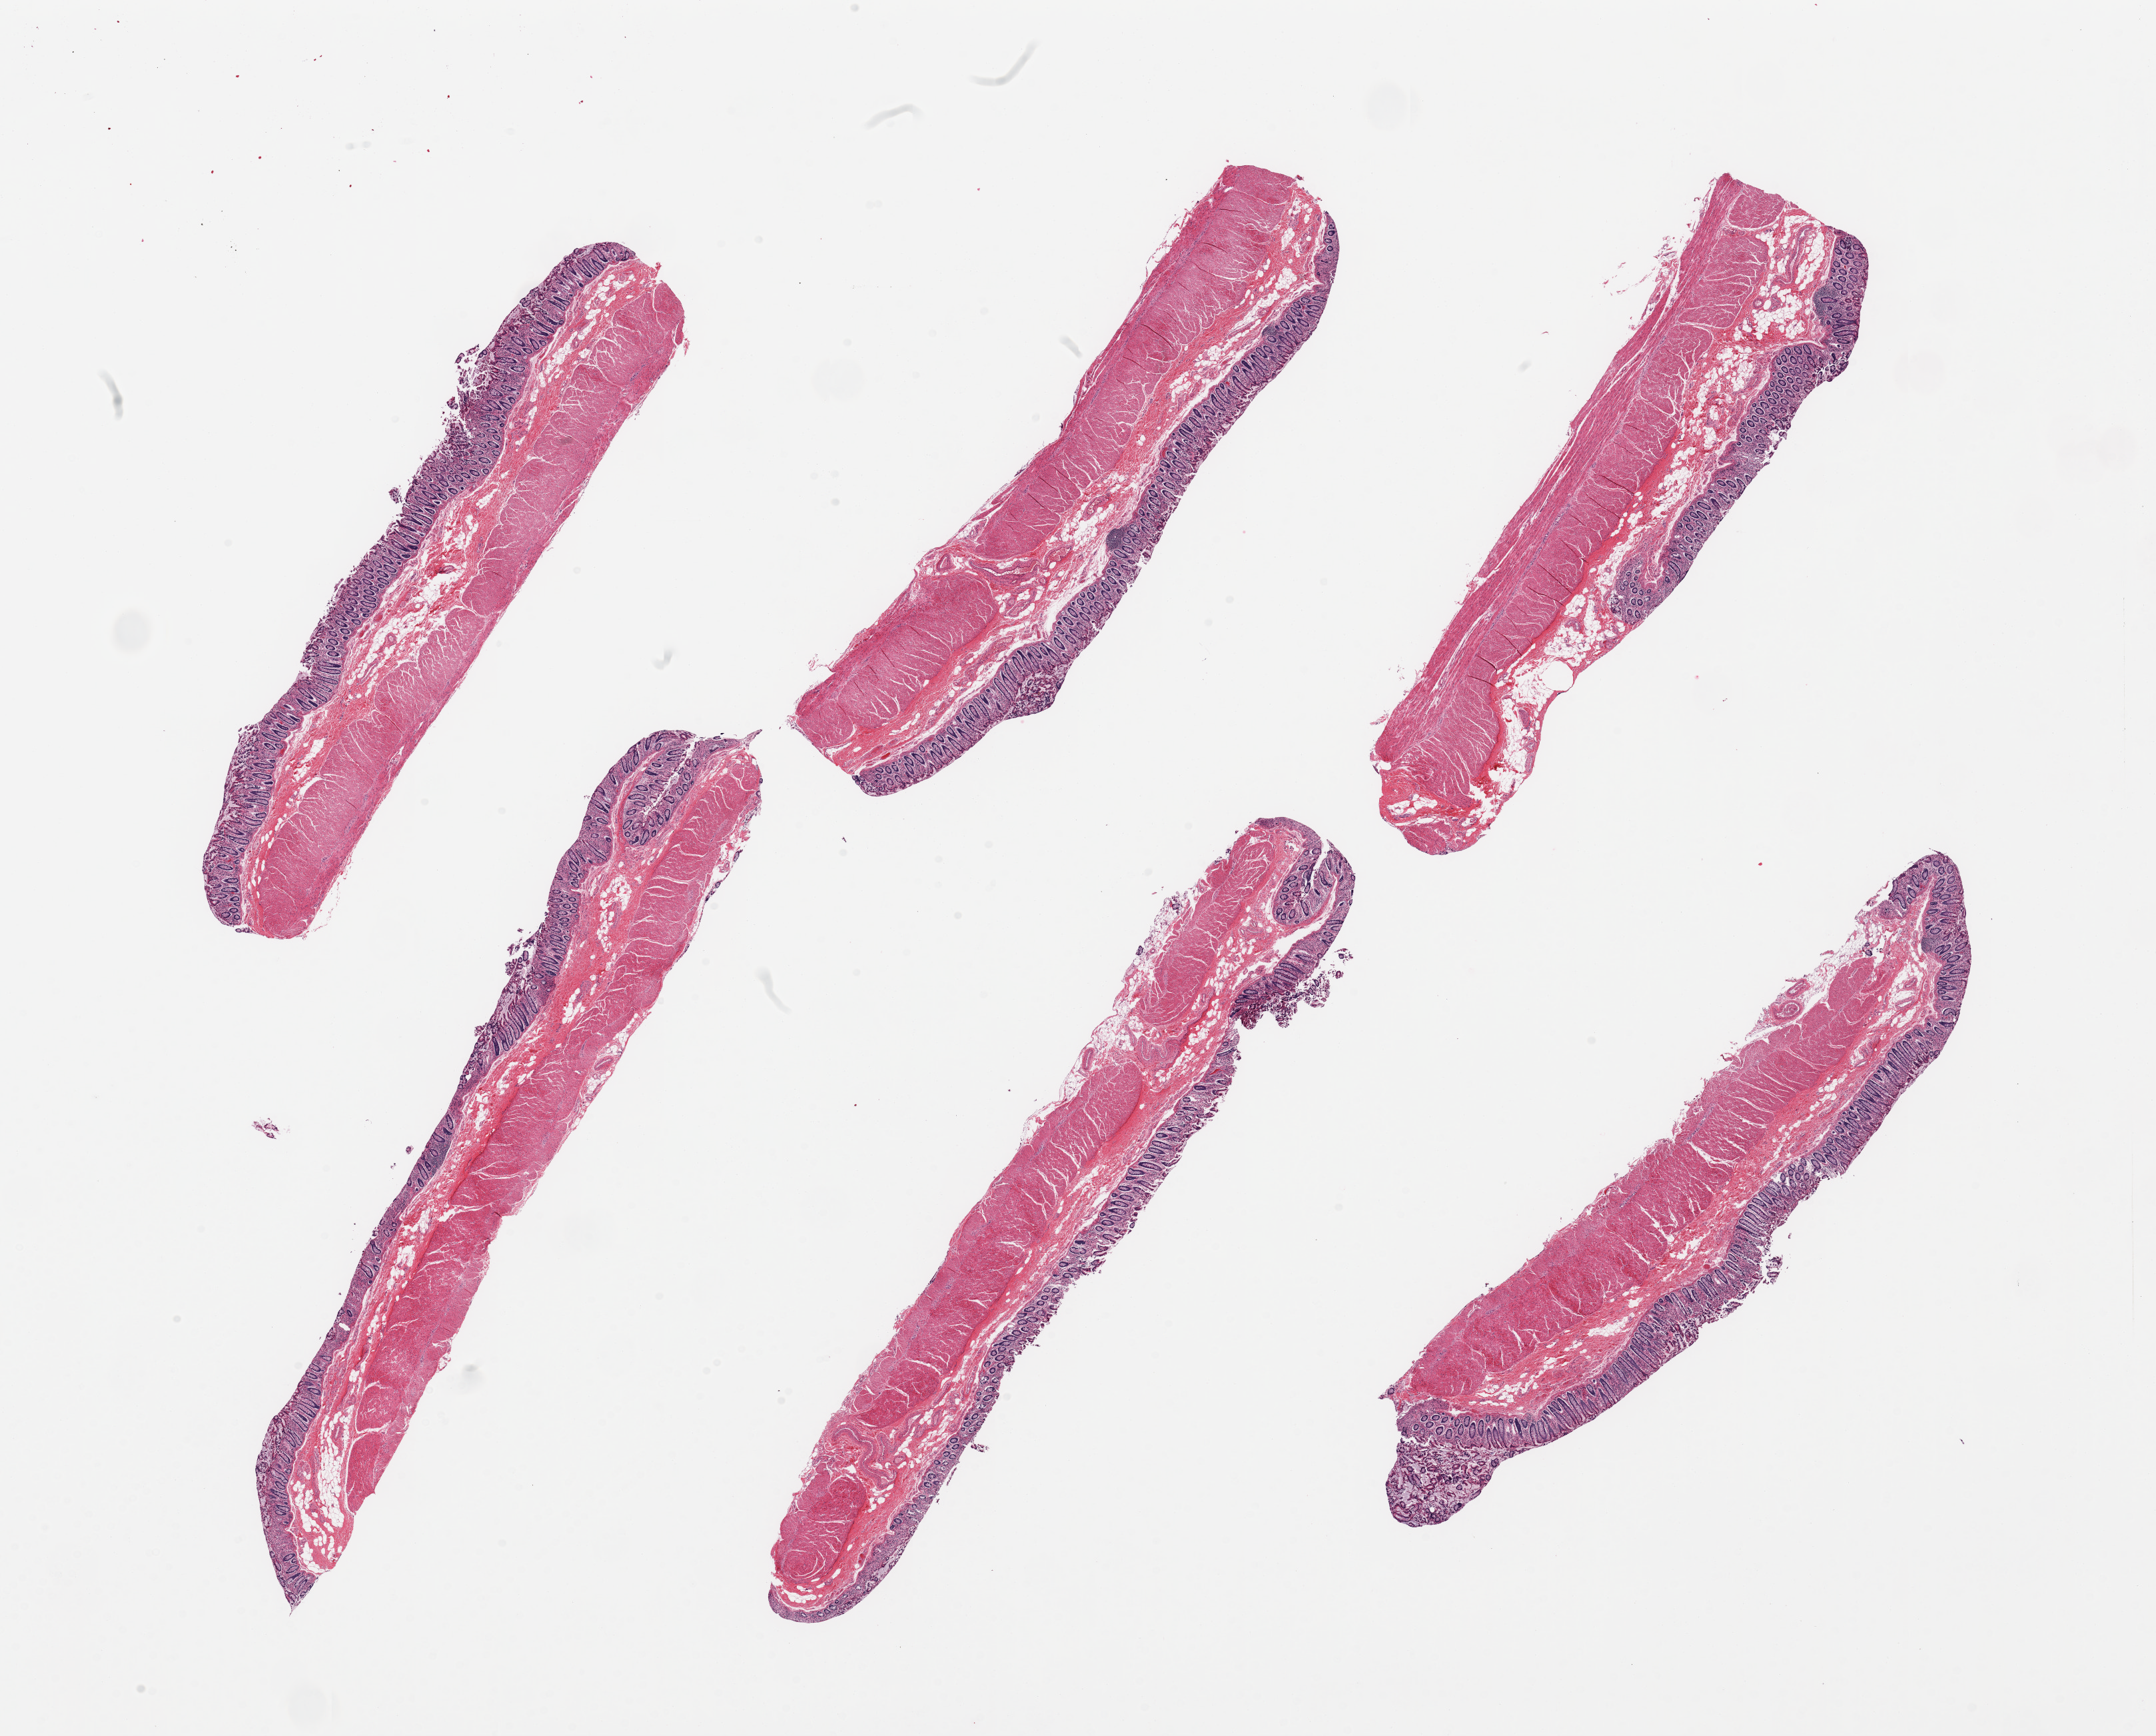
H&E whole-slide image, brightfield — a low-resolution overview of the entire scanned area, about 25.6 x 20.6 mm. PAXgene-fixed, paraffin-embedded tissue. Section of transverse colon (target tissue). Donor tissue sample. Male donor.
Reviewer comment on this tissue sample: 6 pieces, target mucosa is ~0.5mm, ~20% thickness; deeper (basal) mucosa better preserved (score 1).